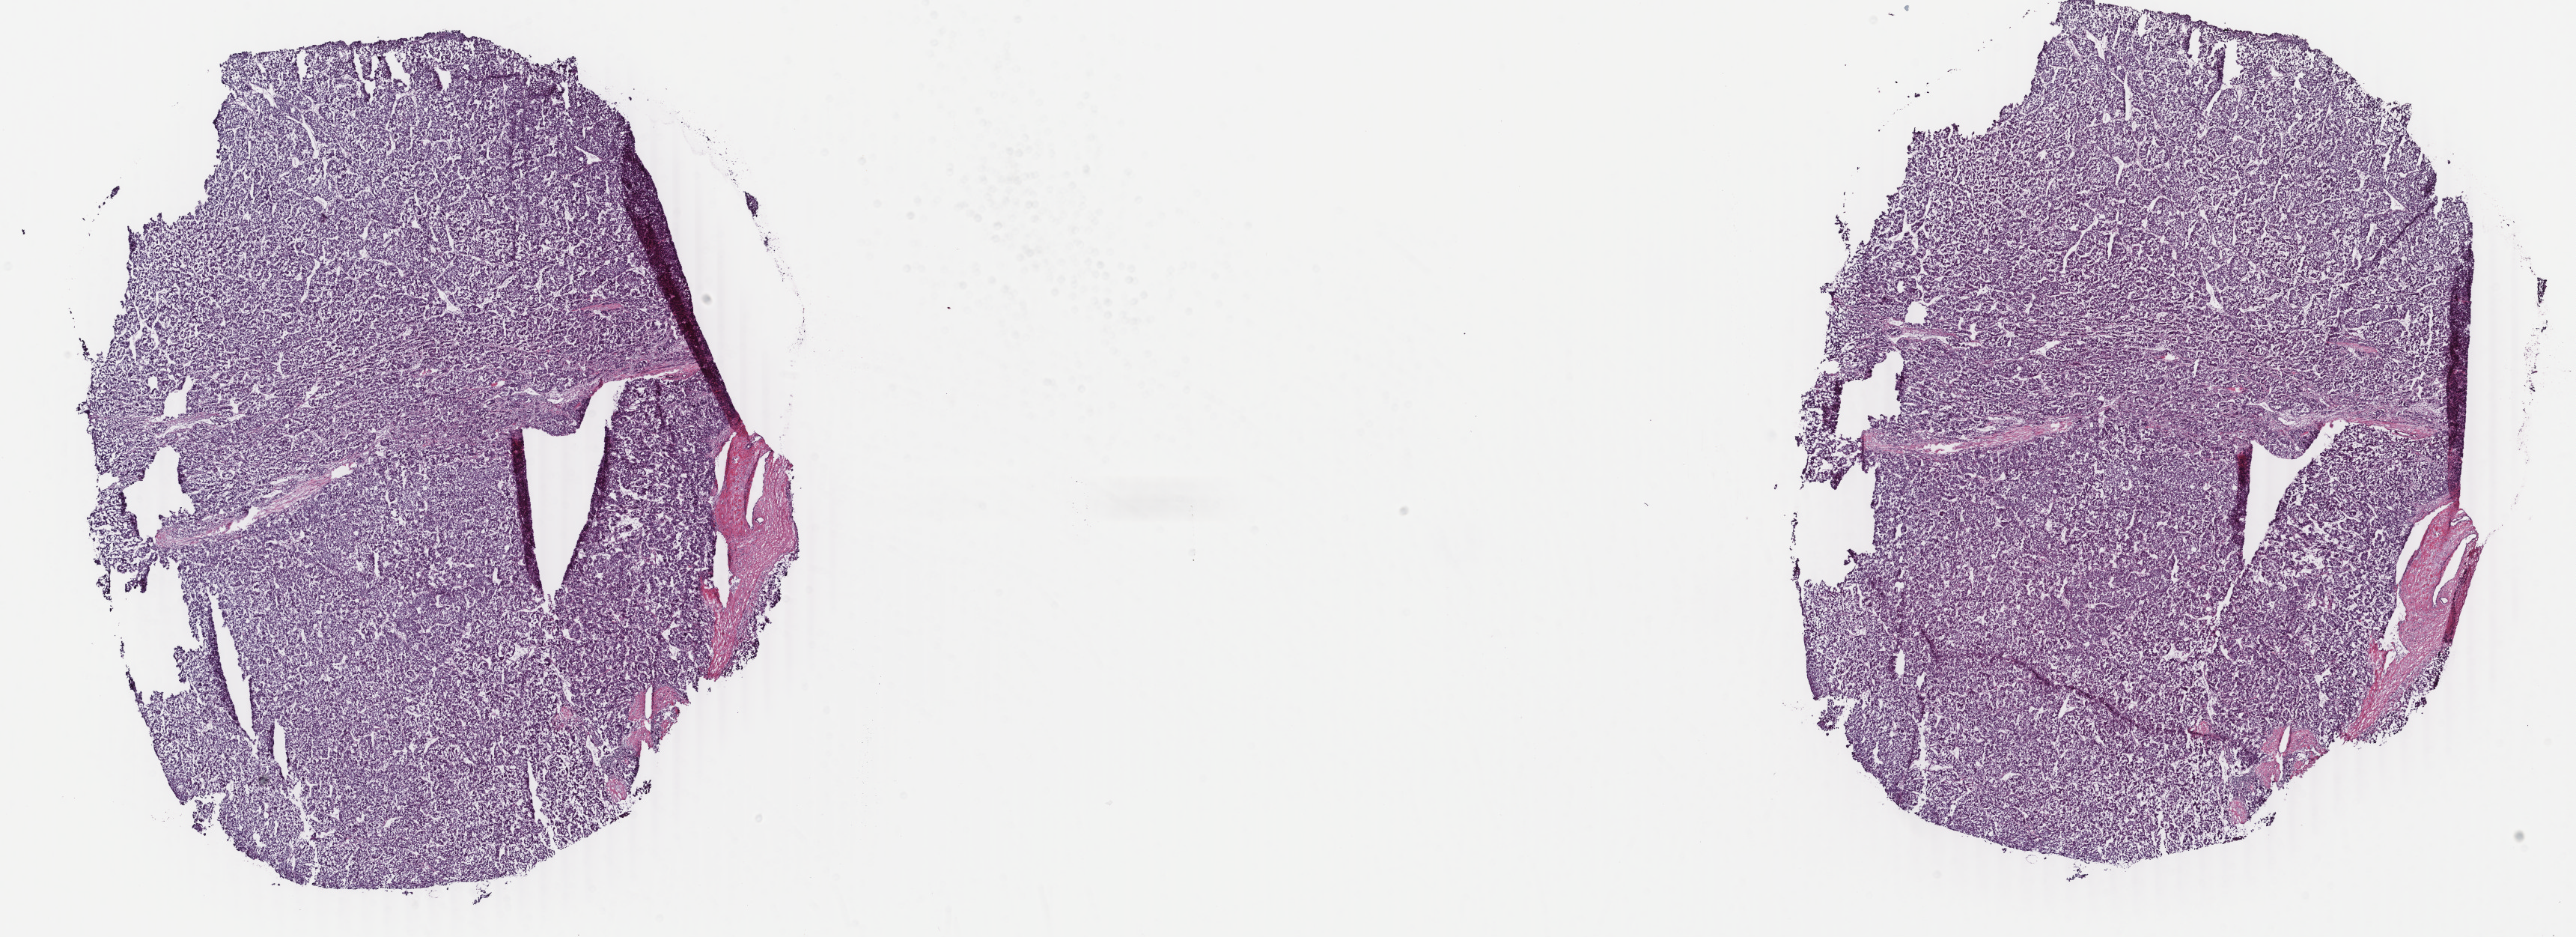
H&E-stained whole-slide image — a low-resolution overview of the entire scanned area, about 27.4 x 9.9 mm. Frozen section. Liver, primary tumour sample. Patient: male, age at initial diagnosis 50 years. Histologic grade: G3 (poorly differentiated). Composition of this section per pathologist review: tumour cells 90%, tumour nuclei 90%, normal cells 0%, stromal cells 10%, necrosis 0%. Inflammatory infiltration, as recorded: lymphocyte infiltration 3%, monocyte infiltration 0%, neutrophil infiltration 0%.
- histologic diagnosis: Hepatocellular carcinoma, NOS